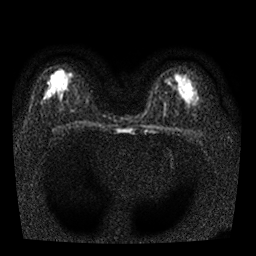
Breast MRI, one axial slice; slice 16 of 25 in the series (ordered by position); diffusion-weighted series; image 2 of 4 stored at this slice position (different b-values; order by instance number); 1.5 T; 4 mm slice thickness; 256 × 256 image matrix, field of view 310 × 310 mm. Female patient.
Outlined on this slice (expert manual segmentation):
- tumour on diffusion-weighted imaging: bounding box <47,81,51,85> (left, top, right, bottom; pixels)